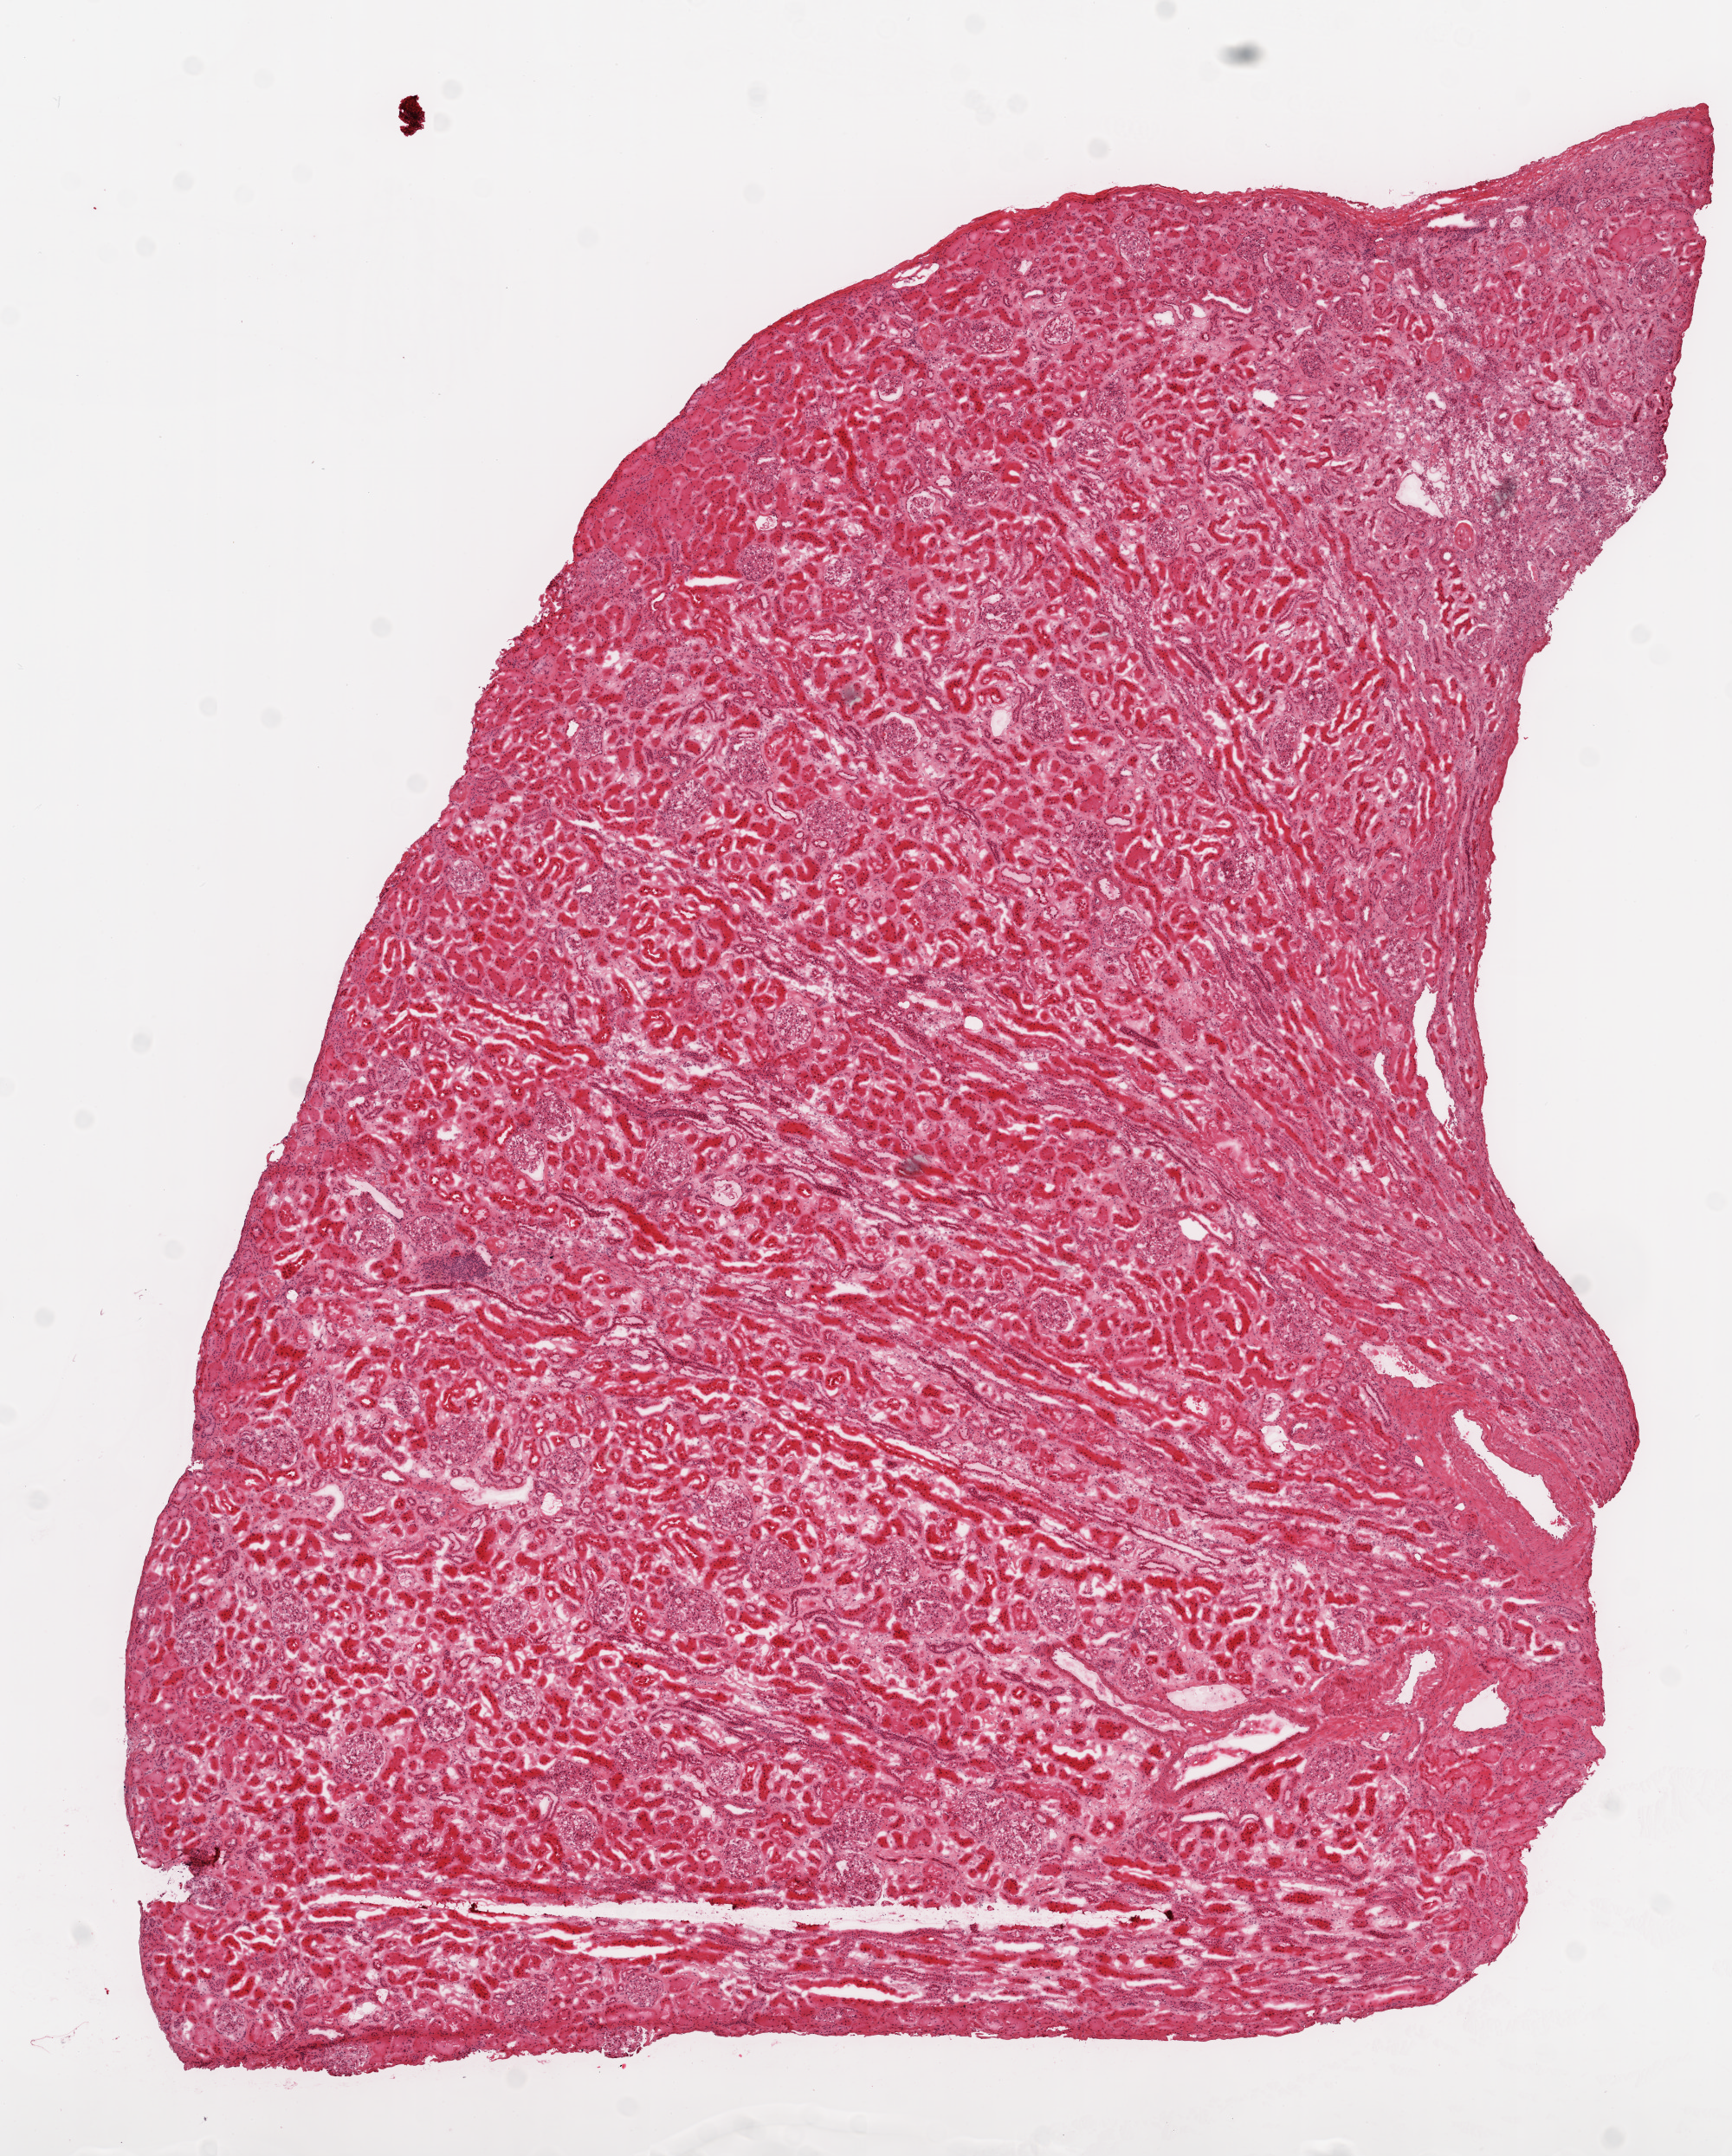
Hematoxylin and eosin (H&E) stained whole-slide image — a low-resolution overview of the entire scanned area, about 8.0 x 10.0 mm; frozen section; solid tissue normal (non-tumour tissue) sample from the kidney. Patient: male, age at initial diagnosis 54 years.
* this section: solid tissue normal (non-tumour) sample from the same patient
* patient diagnosis: Clear cell adenocarcinoma, NOS